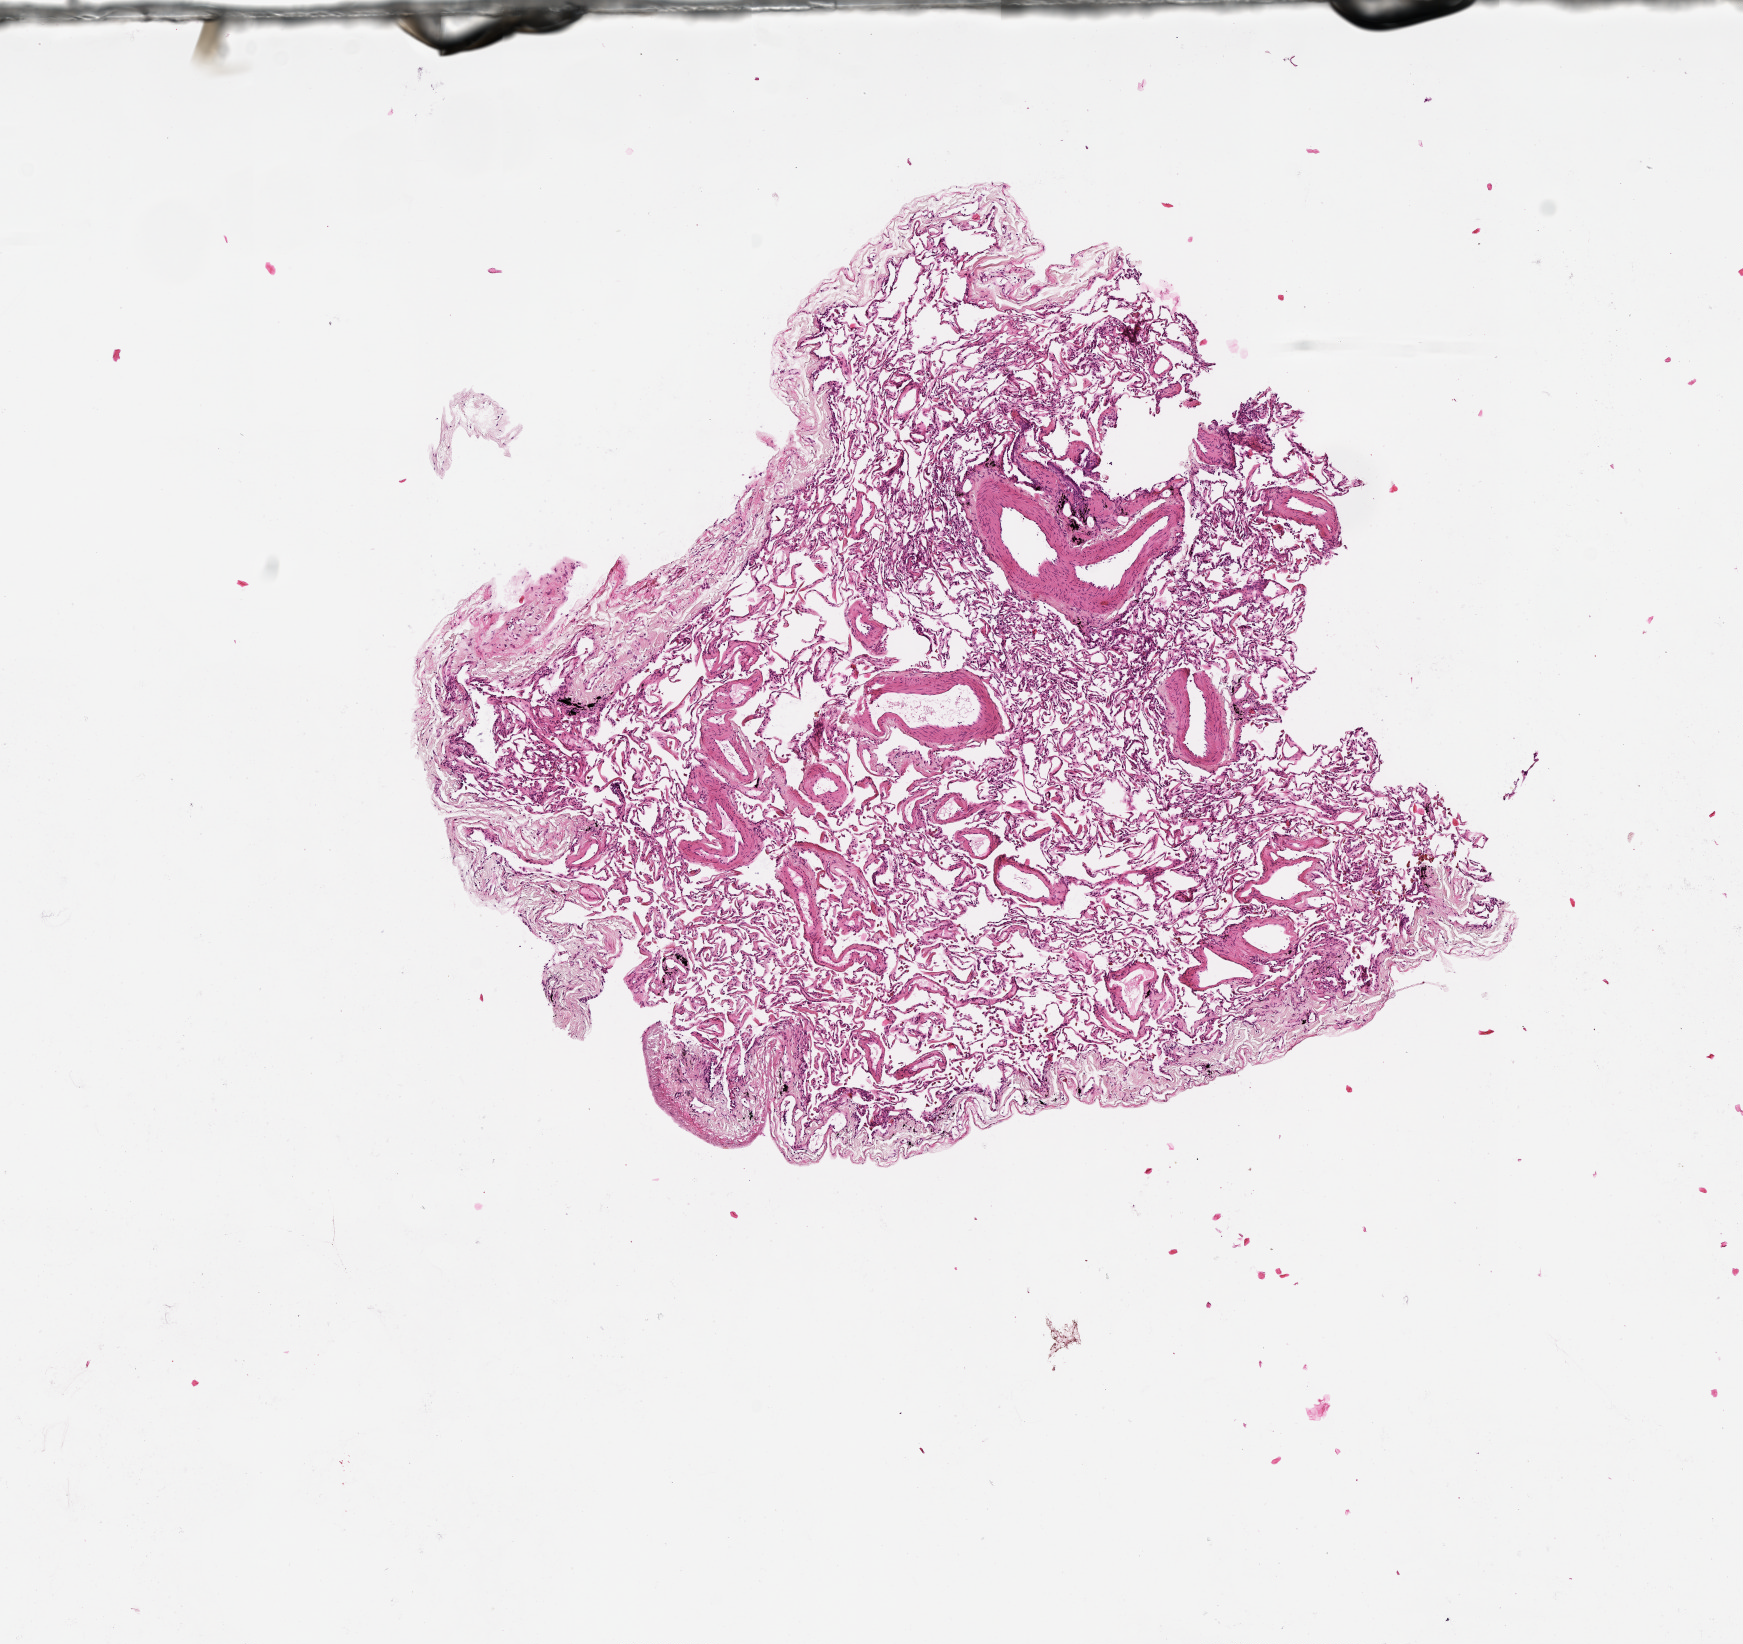
Digitized H&E-stained tissue section (whole slide), shown as a low-resolution overview of the whole scanned area (about 7.0 x 6.6 mm, from a 20x scan), normal (non-tumour) tissue sample, lung. Male, 64 y/o.
This section: normal (non-tumour) tissue from the same patient. Patient diagnosis (cohort enrolment): squamous cell carcinoma (lung).